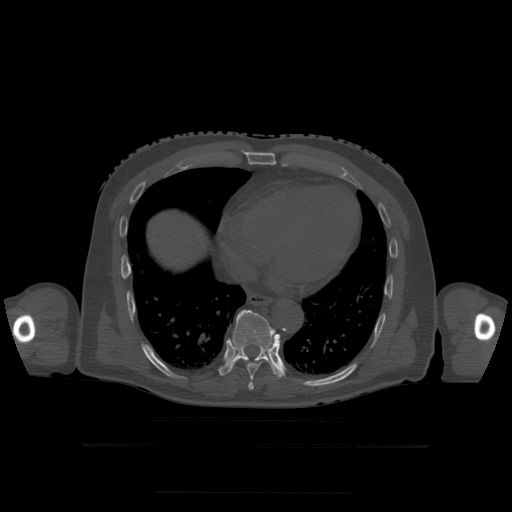
CT including the spine, one axial slice. Slice 270 of 522 in the series (ordered by position). Bone window (W 1800 / L 400 HU). 1.25 mm slice thickness. 512 × 512 image matrix, field of view 436 × 436 mm. Patient age 68 years. From the clinical record (not read from this slice): primary cancer: urothelial.
Annotated regions visible in this slice (semi-automatic segmentation, software-assisted and operator-edited):
- T7 vertebra: box from (x=248, y=382) to (x=254, y=390) px
- T8 vertebra: (x=246, y=358)–(x=272, y=381)
- T9 vertebra: (x=220, y=310)–(x=284, y=378)